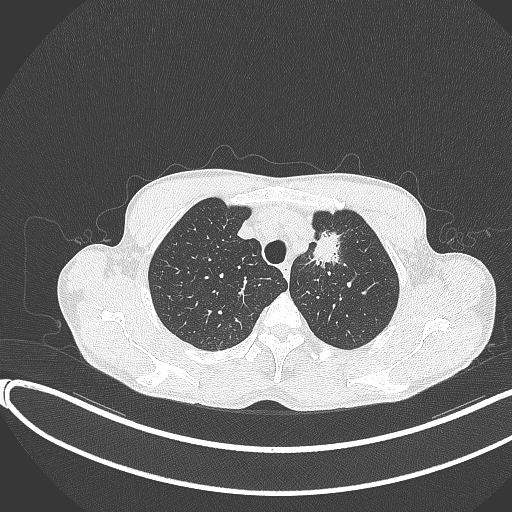
Chest CT, one axial slice. Position 316 of 374 along the scan axis. Reconstruction kernel B70f. 120 kVp. Lung window (W 1500 / L -600 HU). 1 mm slice thickness. 512 × 512 image matrix, field of view 400 × 400 mm. Male patient, age 58 years. Case-level facts recorded for this patient, not image findings: clinical TNM (as recorded): T1c N1 M0.
Annotated regions visible in this slice (bounding box drawn by a radiologist):
- lung tumour (recorded histology: adenocarcinoma): box from (x=306, y=227) to (x=346, y=279) px